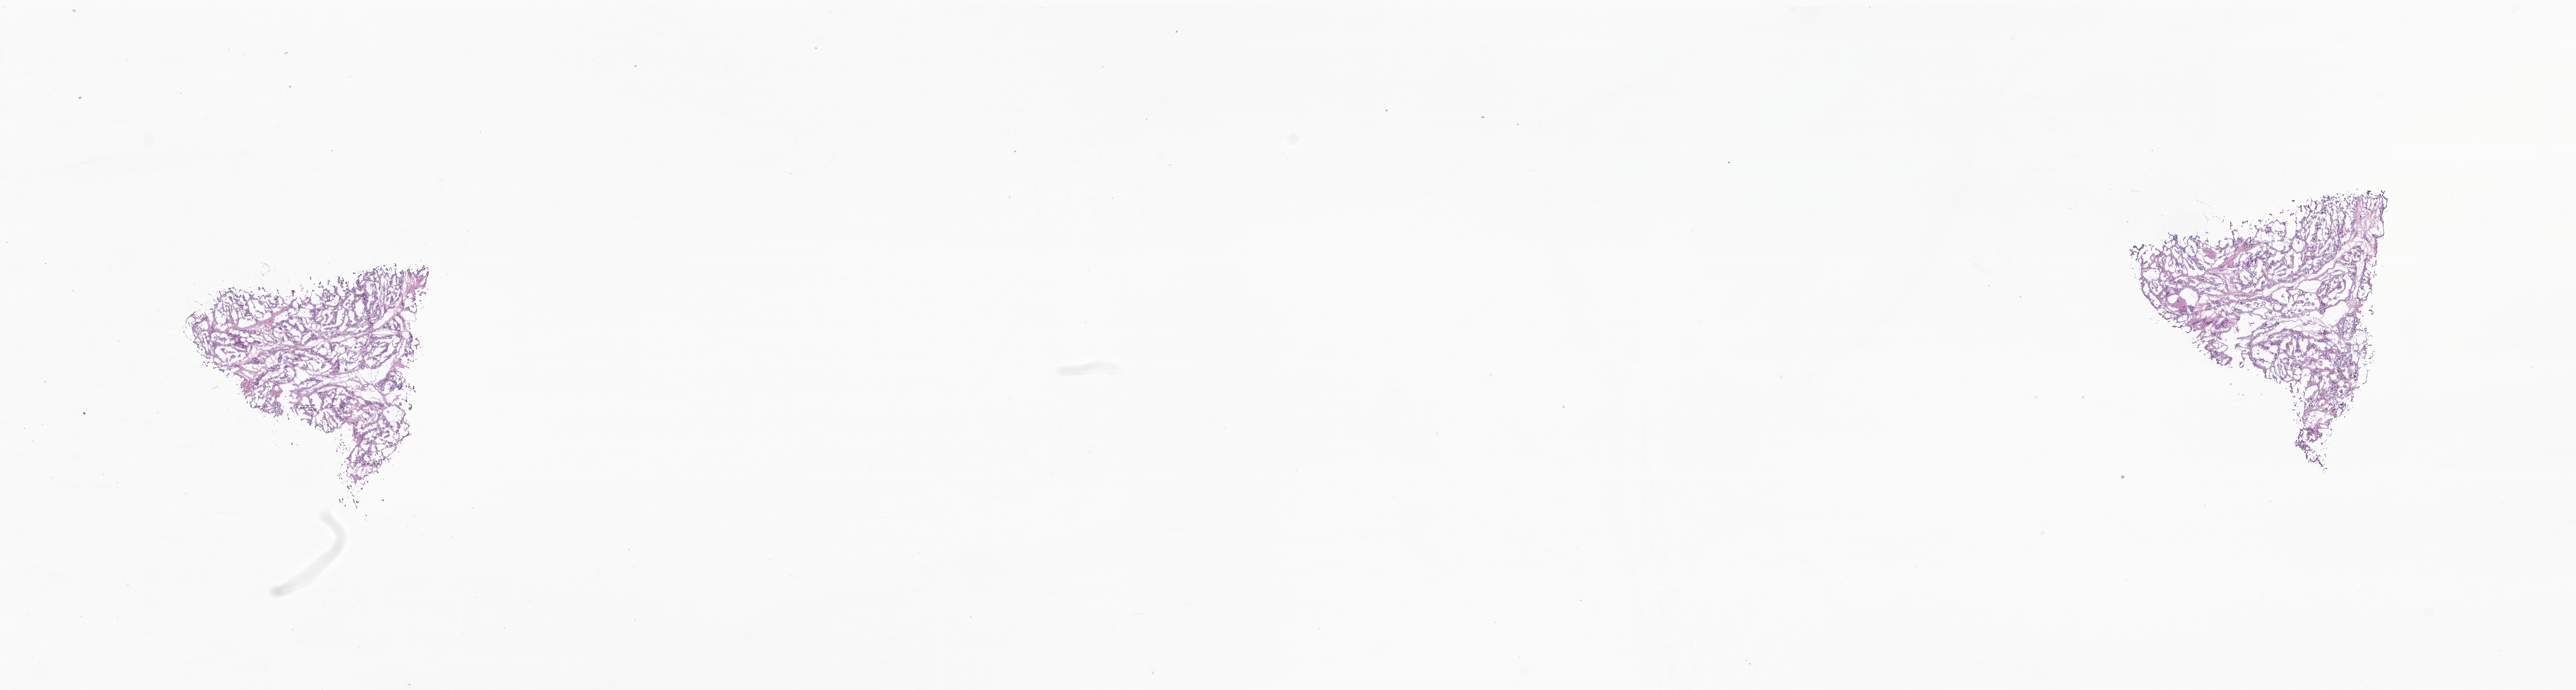
Whole-slide image, H&E stain of tumor tissue from the thyroid — shown as a low-resolution overview of the whole scanned area (about 25.4 x 6.8 mm), frozen section. Patient: female, age 183 months (15 years 3 months).
Recorded diagnosis: Papillary adenocarcinoma, NOS.